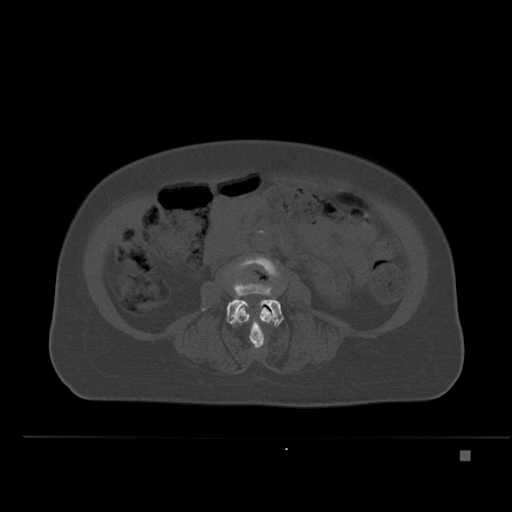
CT including the spine, one axial slice; slice 187 of 477 in the series (ordered by position); bone window (W 1800 / L 400 HU); 512 × 512 image matrix, field of view 422 × 422 mm. Patient: female, 74 years. From the clinical record (not read from this slice): primary cancer: colon.
Structures marked on this image (semi-automatic segmentation, software-assisted and operator-edited):
- L3 vertebra: box from (x=227, y=255) to (x=281, y=349) px
- L4 vertebra: (x=226, y=280)–(x=284, y=326)